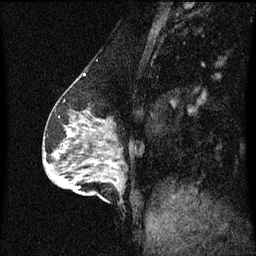
Breast MRI (dynamic contrast-enhanced), one sagittal slice. Position 21 of 60 along the scan axis. Dynamic contrast-enhanced series, image 2 of 3 at this slice position (ordered by acquisition). 1.5 T. TE 4.2 ms, TR 8.4 ms. 2 mm slice thickness. 256 × 256 image matrix. Patient: female, 64 years.
Structures marked on this image (semi-automatic segmentation, software-assisted and operator-edited):
- analysis volume of interest (the breast-tissue region the enhancement analysis was run in; not a lesion): bounding box [x1, y1, x2, y2] px = [90, 164, 125, 203]
- tumour enhancement mask (voxels above the 70 % enhancement threshold inside the analysis volume of interest): [116, 168, 117, 173]